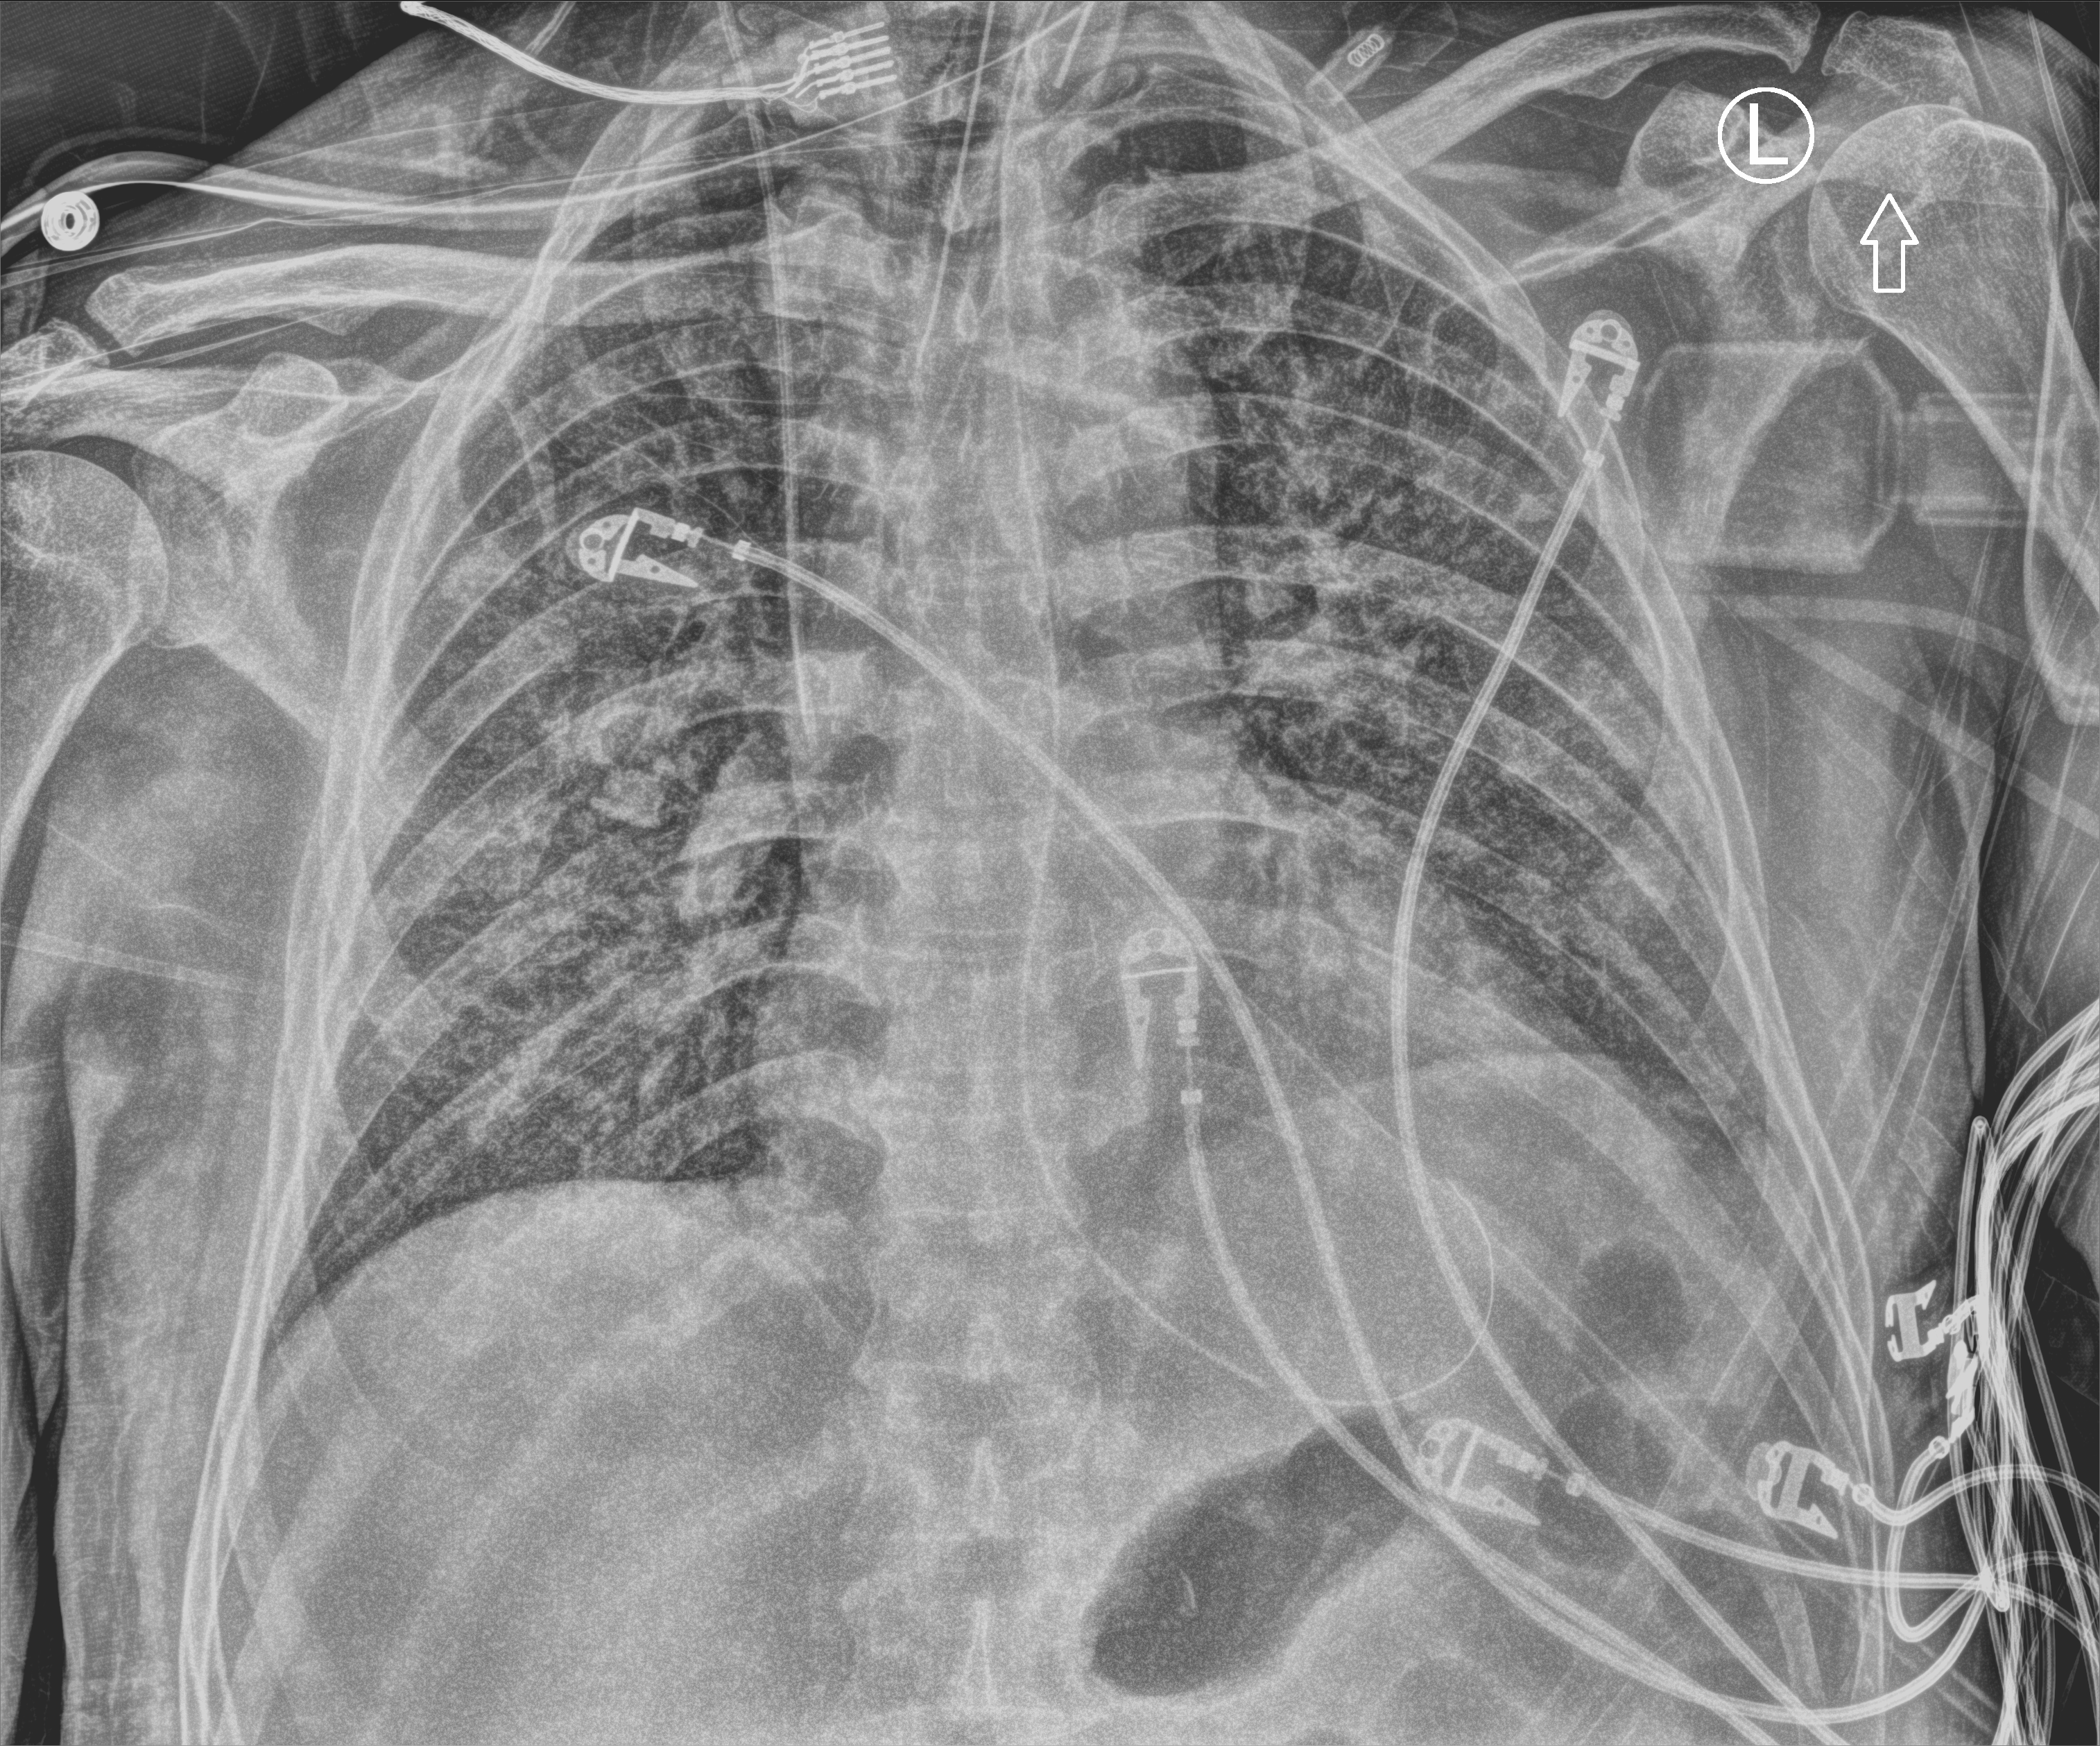
Chest X-ray (portable), anteroposterior (AP) projection. Male patient hospitalised with COVID-19, age 60–74 years.
Hospital-stay facts (about this admission, not read from this image; timing relative to this image not recorded): mechanically ventilated during this hospital stay: yes.